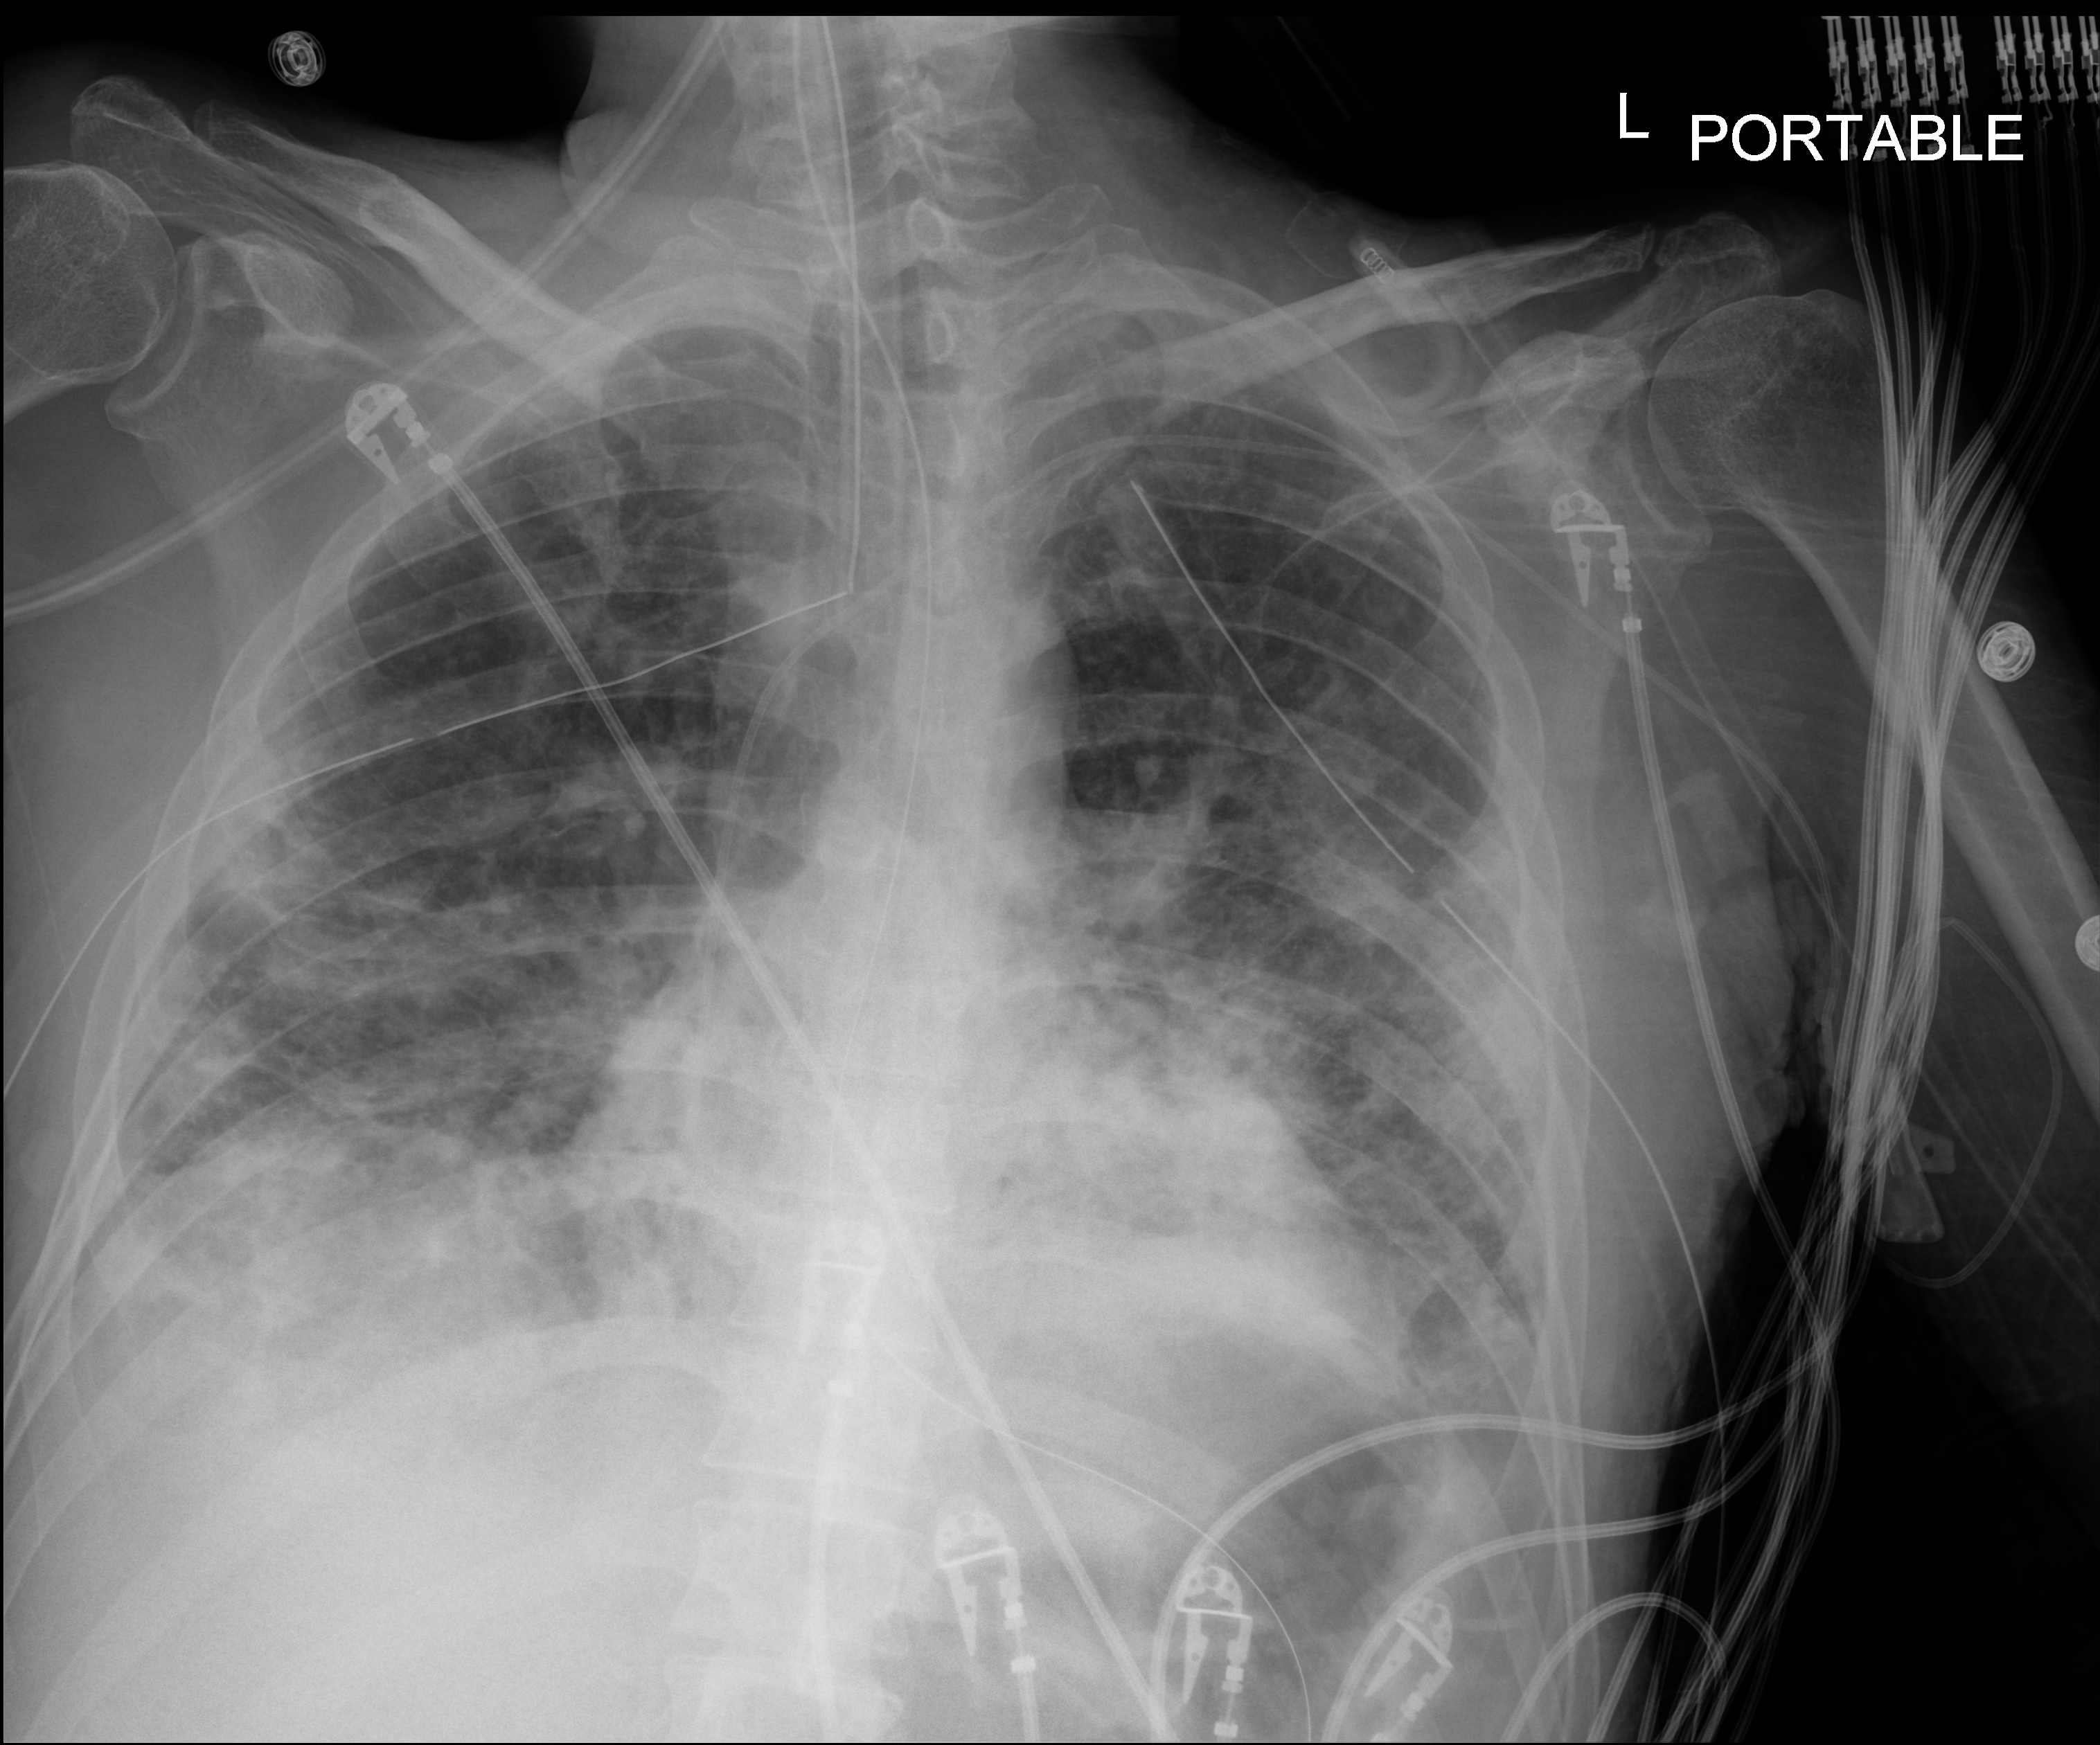
Portable chest radiograph, anteroposterior (AP) projection. Male patient hospitalised with COVID-19, age 18–59 years.
Hospital-stay facts (about this admission, not read from this image; timing relative to this image not recorded):
- hypertension (admission record): yes
- mechanically ventilated during this hospital stay: yes